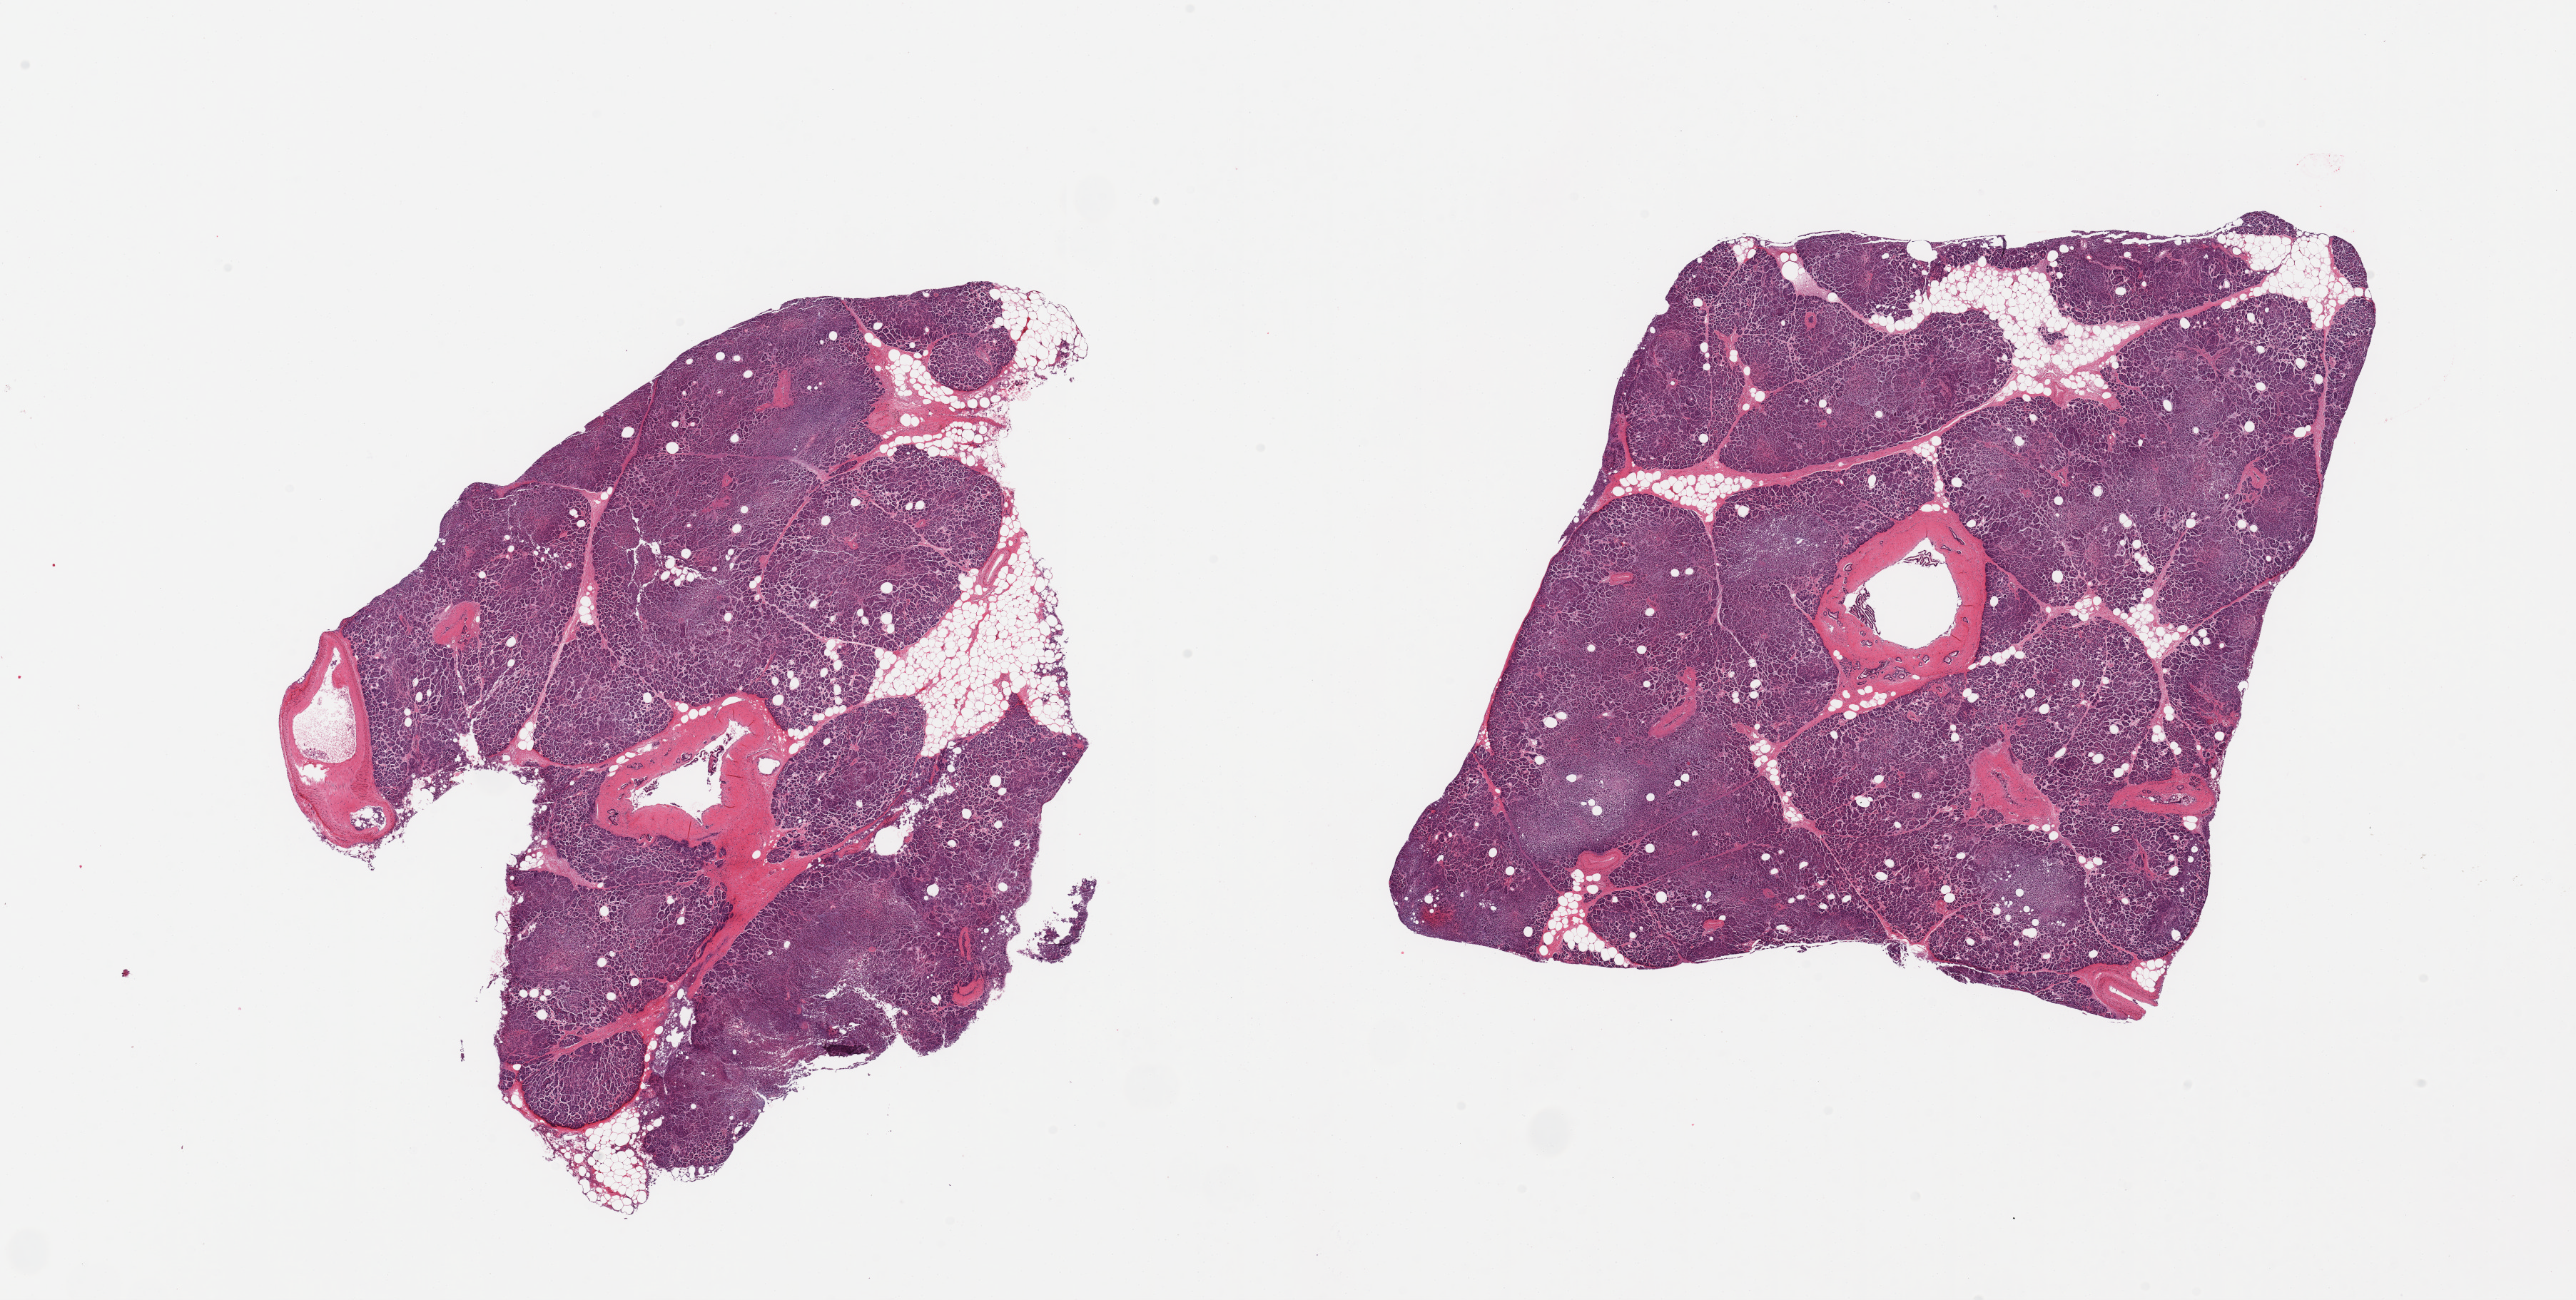
Haematoxylin and eosin whole-slide image — shown as a low-resolution overview of the whole scanned area (about 28.5 x 14.4 mm). PAXgene-fixed, paraffin-embedded tissue. Target tissue: pancreas. Donor tissue sample.
* review note (as recorded): 2 pieces, moderate saponfication; islets not well visualized